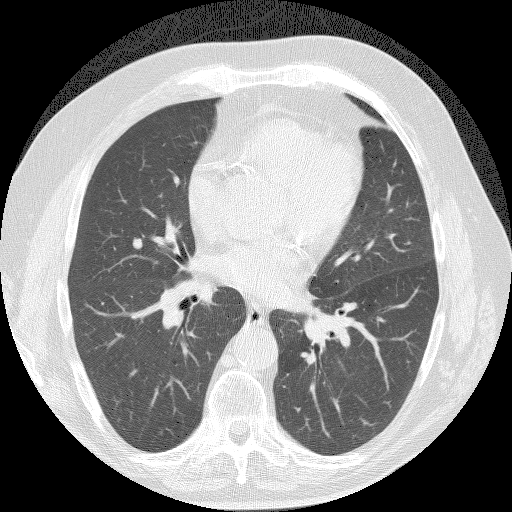
Chest CT (low-dose screening protocol), one axial image, baseline screening round, lung window (W 1500 / L -600 HU), 2.5 mm slice thickness. Male, age 61 years at enrolment. Current smoker at enrolment.
• Expert-annotated lung lesion, bounding box <109,225,155,263> (left, top, right, bottom; pixels).
• The screening reader recorded 3 non-calcified nodules or masses ≥4 mm on this exam; which of them this box marks is not recorded.
• Official screen result: positive, change unspecified: nodule(s) >= 4 mm or enlarging nodule(s), mass(es), or other non-specific abnormalities suspicious for lung cancer.
• Participant outcome: lung cancer diagnosed 491 days after this screen (after the second annual screen) — bronchiolo-alveolar adenocarcinoma, NOS, right middle lobe, well differentiated (G1), stage IA (AJCC 6th edition), 15 mm at pathology.